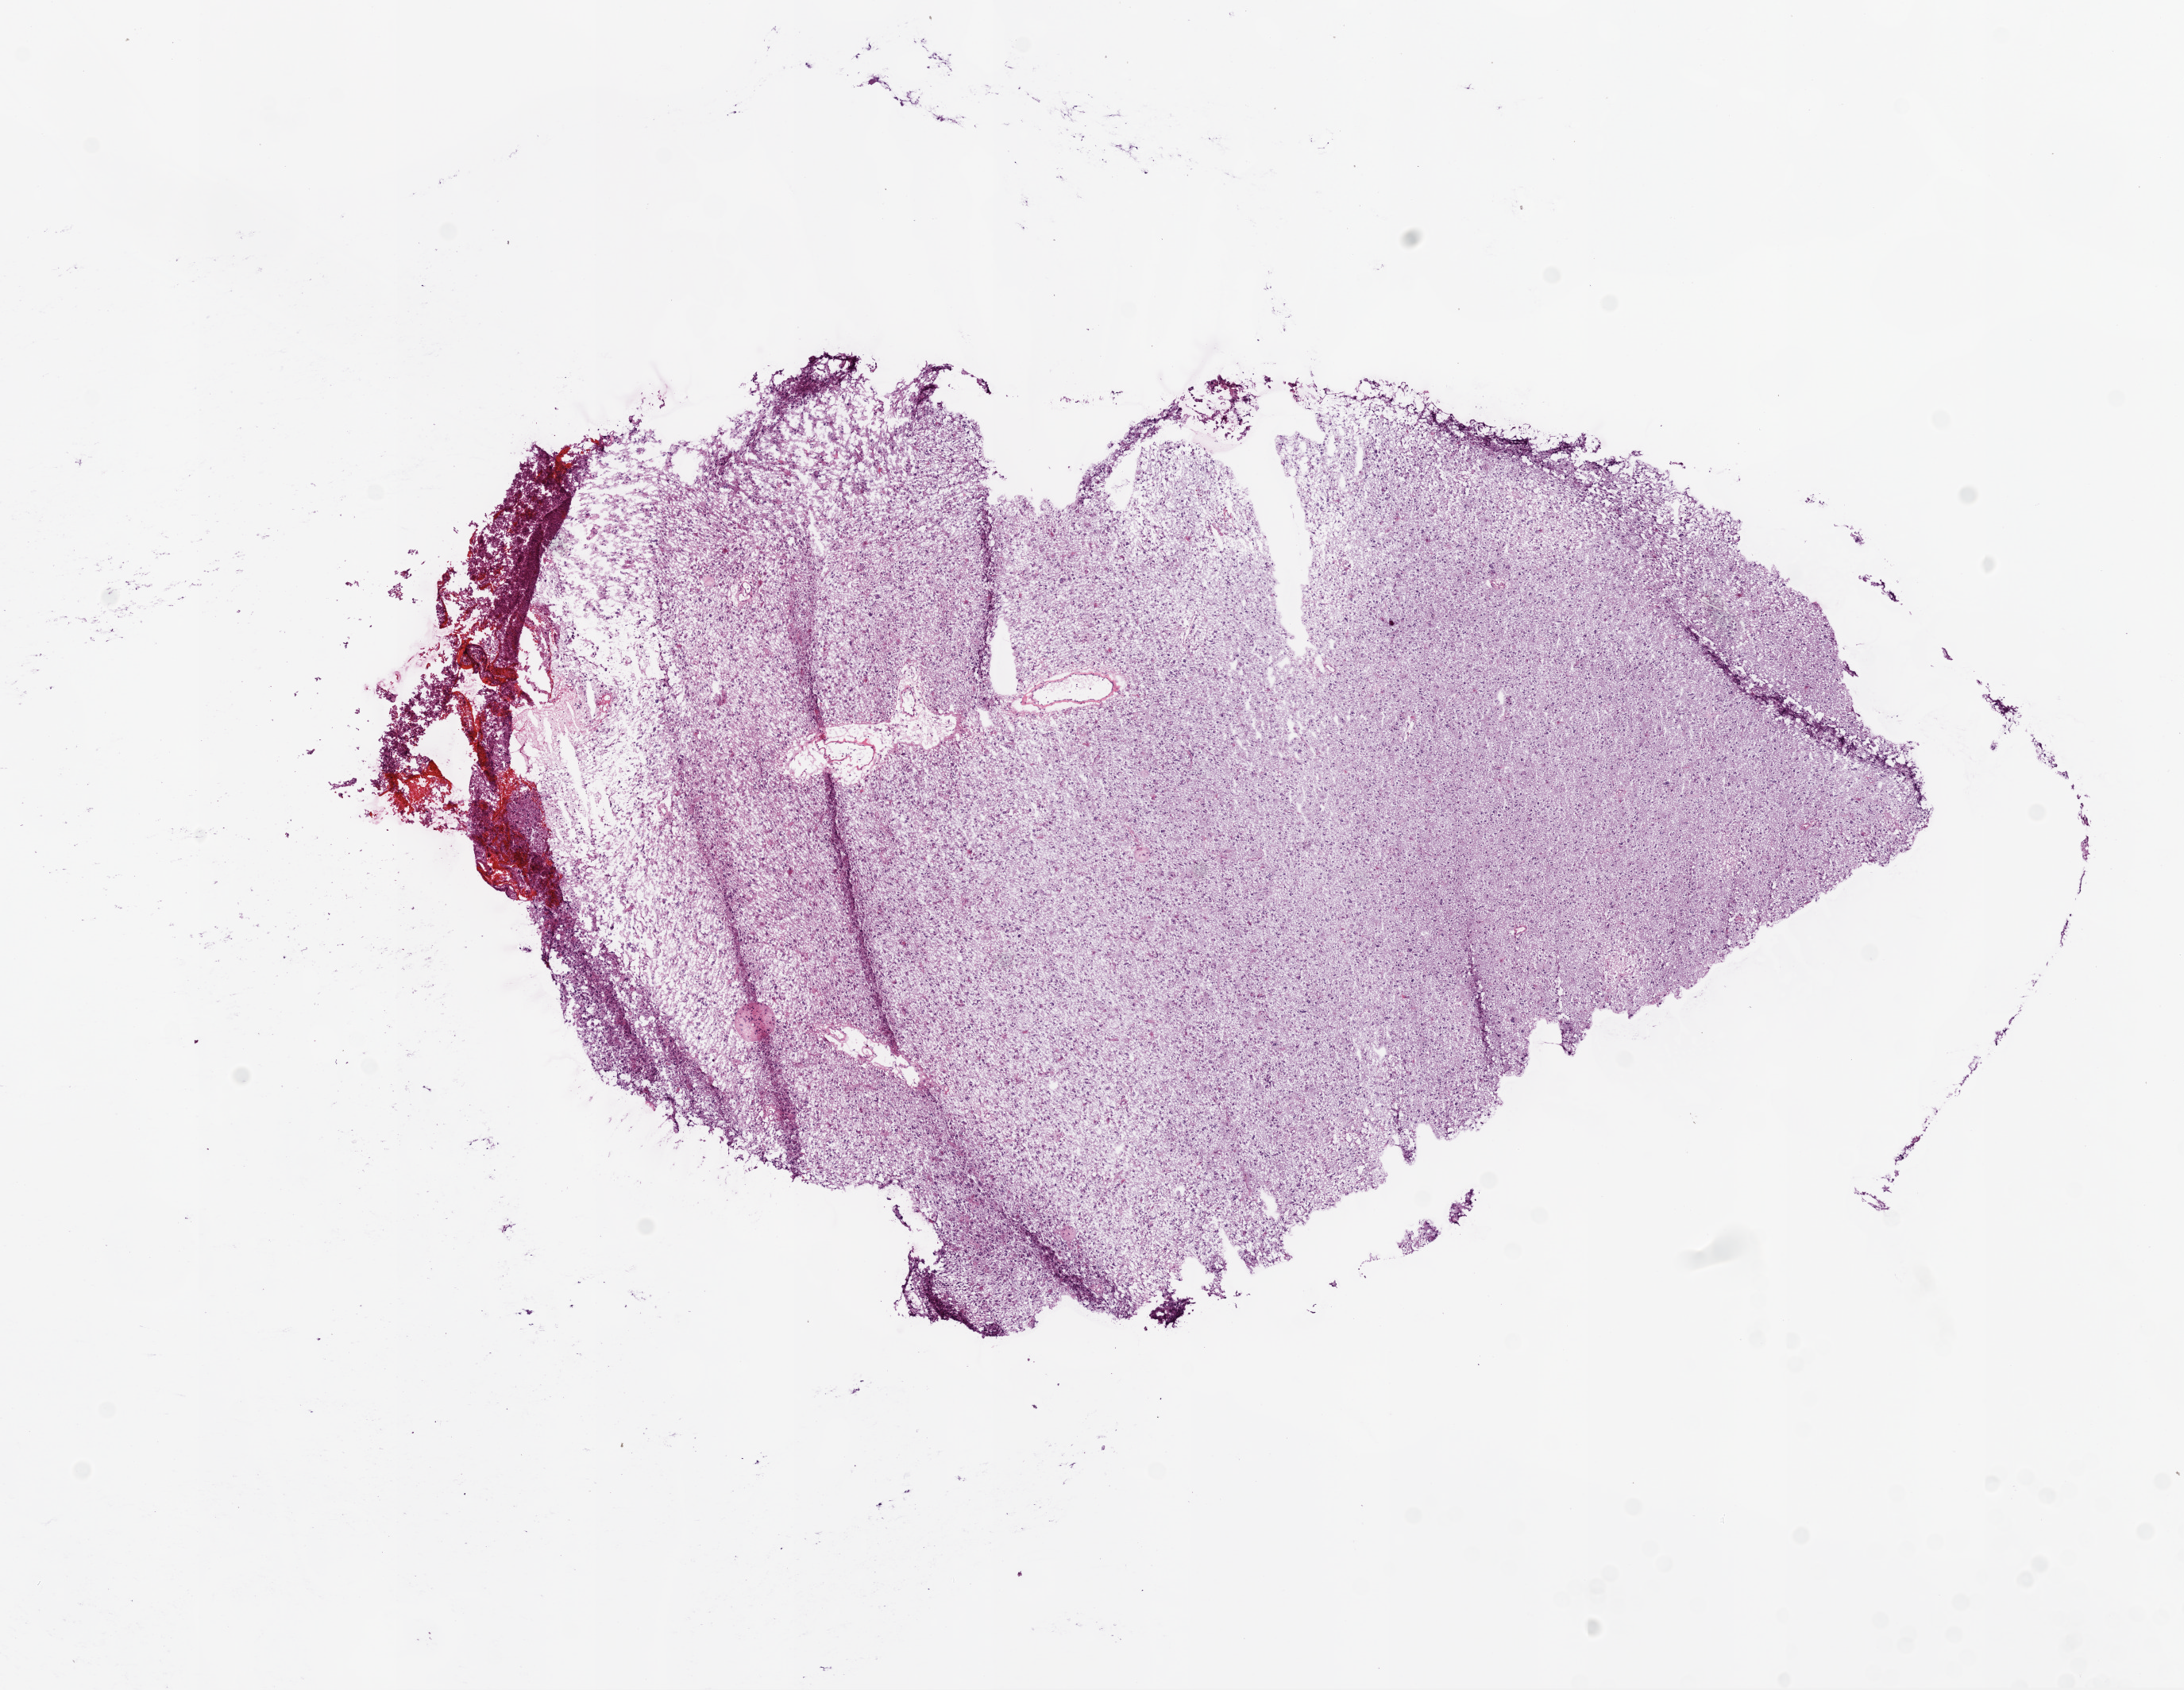
Whole-slide histology image, Hematoxylin and eosin (H&E) stained — a low-resolution overview of the entire scanned area, about 11.0 x 8.5 mm; frozen section from the bottom of the tissue portion; brain, primary tumour sample. Male, age 78 years at initial diagnosis. Composition of this section per pathologist review: tumour cells 100%, tumour nuclei 80%, normal cells 0%, stromal cells 0%, necrosis 0%.
- histologic diagnosis: Glioblastoma